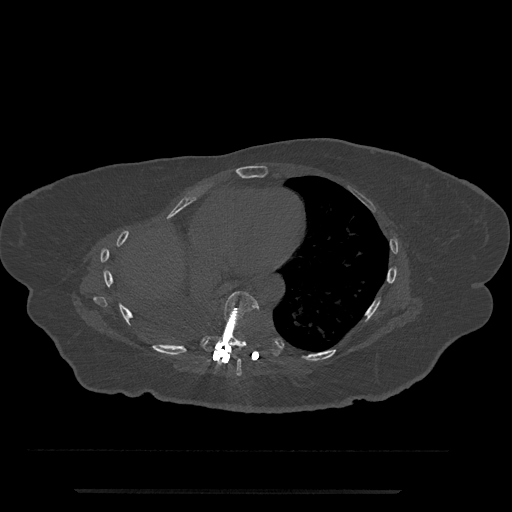
CT including the spine, one axial slice; reconstruction kernel Br40s/3; bone window (W 1800 / L 400 HU); 0.5 mm slice thickness; 512 × 512 image matrix, field of view 440 × 440 mm. Patient: female, 51 years. From the clinical record (not read from this slice): primary cancer: neuro.
Annotated regions visible in this slice (semi-automatic segmentation, software-assisted and operator-edited):
- T7 vertebra: box from (x=233, y=360) to (x=242, y=376) px
- T8 vertebra: (x=201, y=291)–(x=260, y=352)